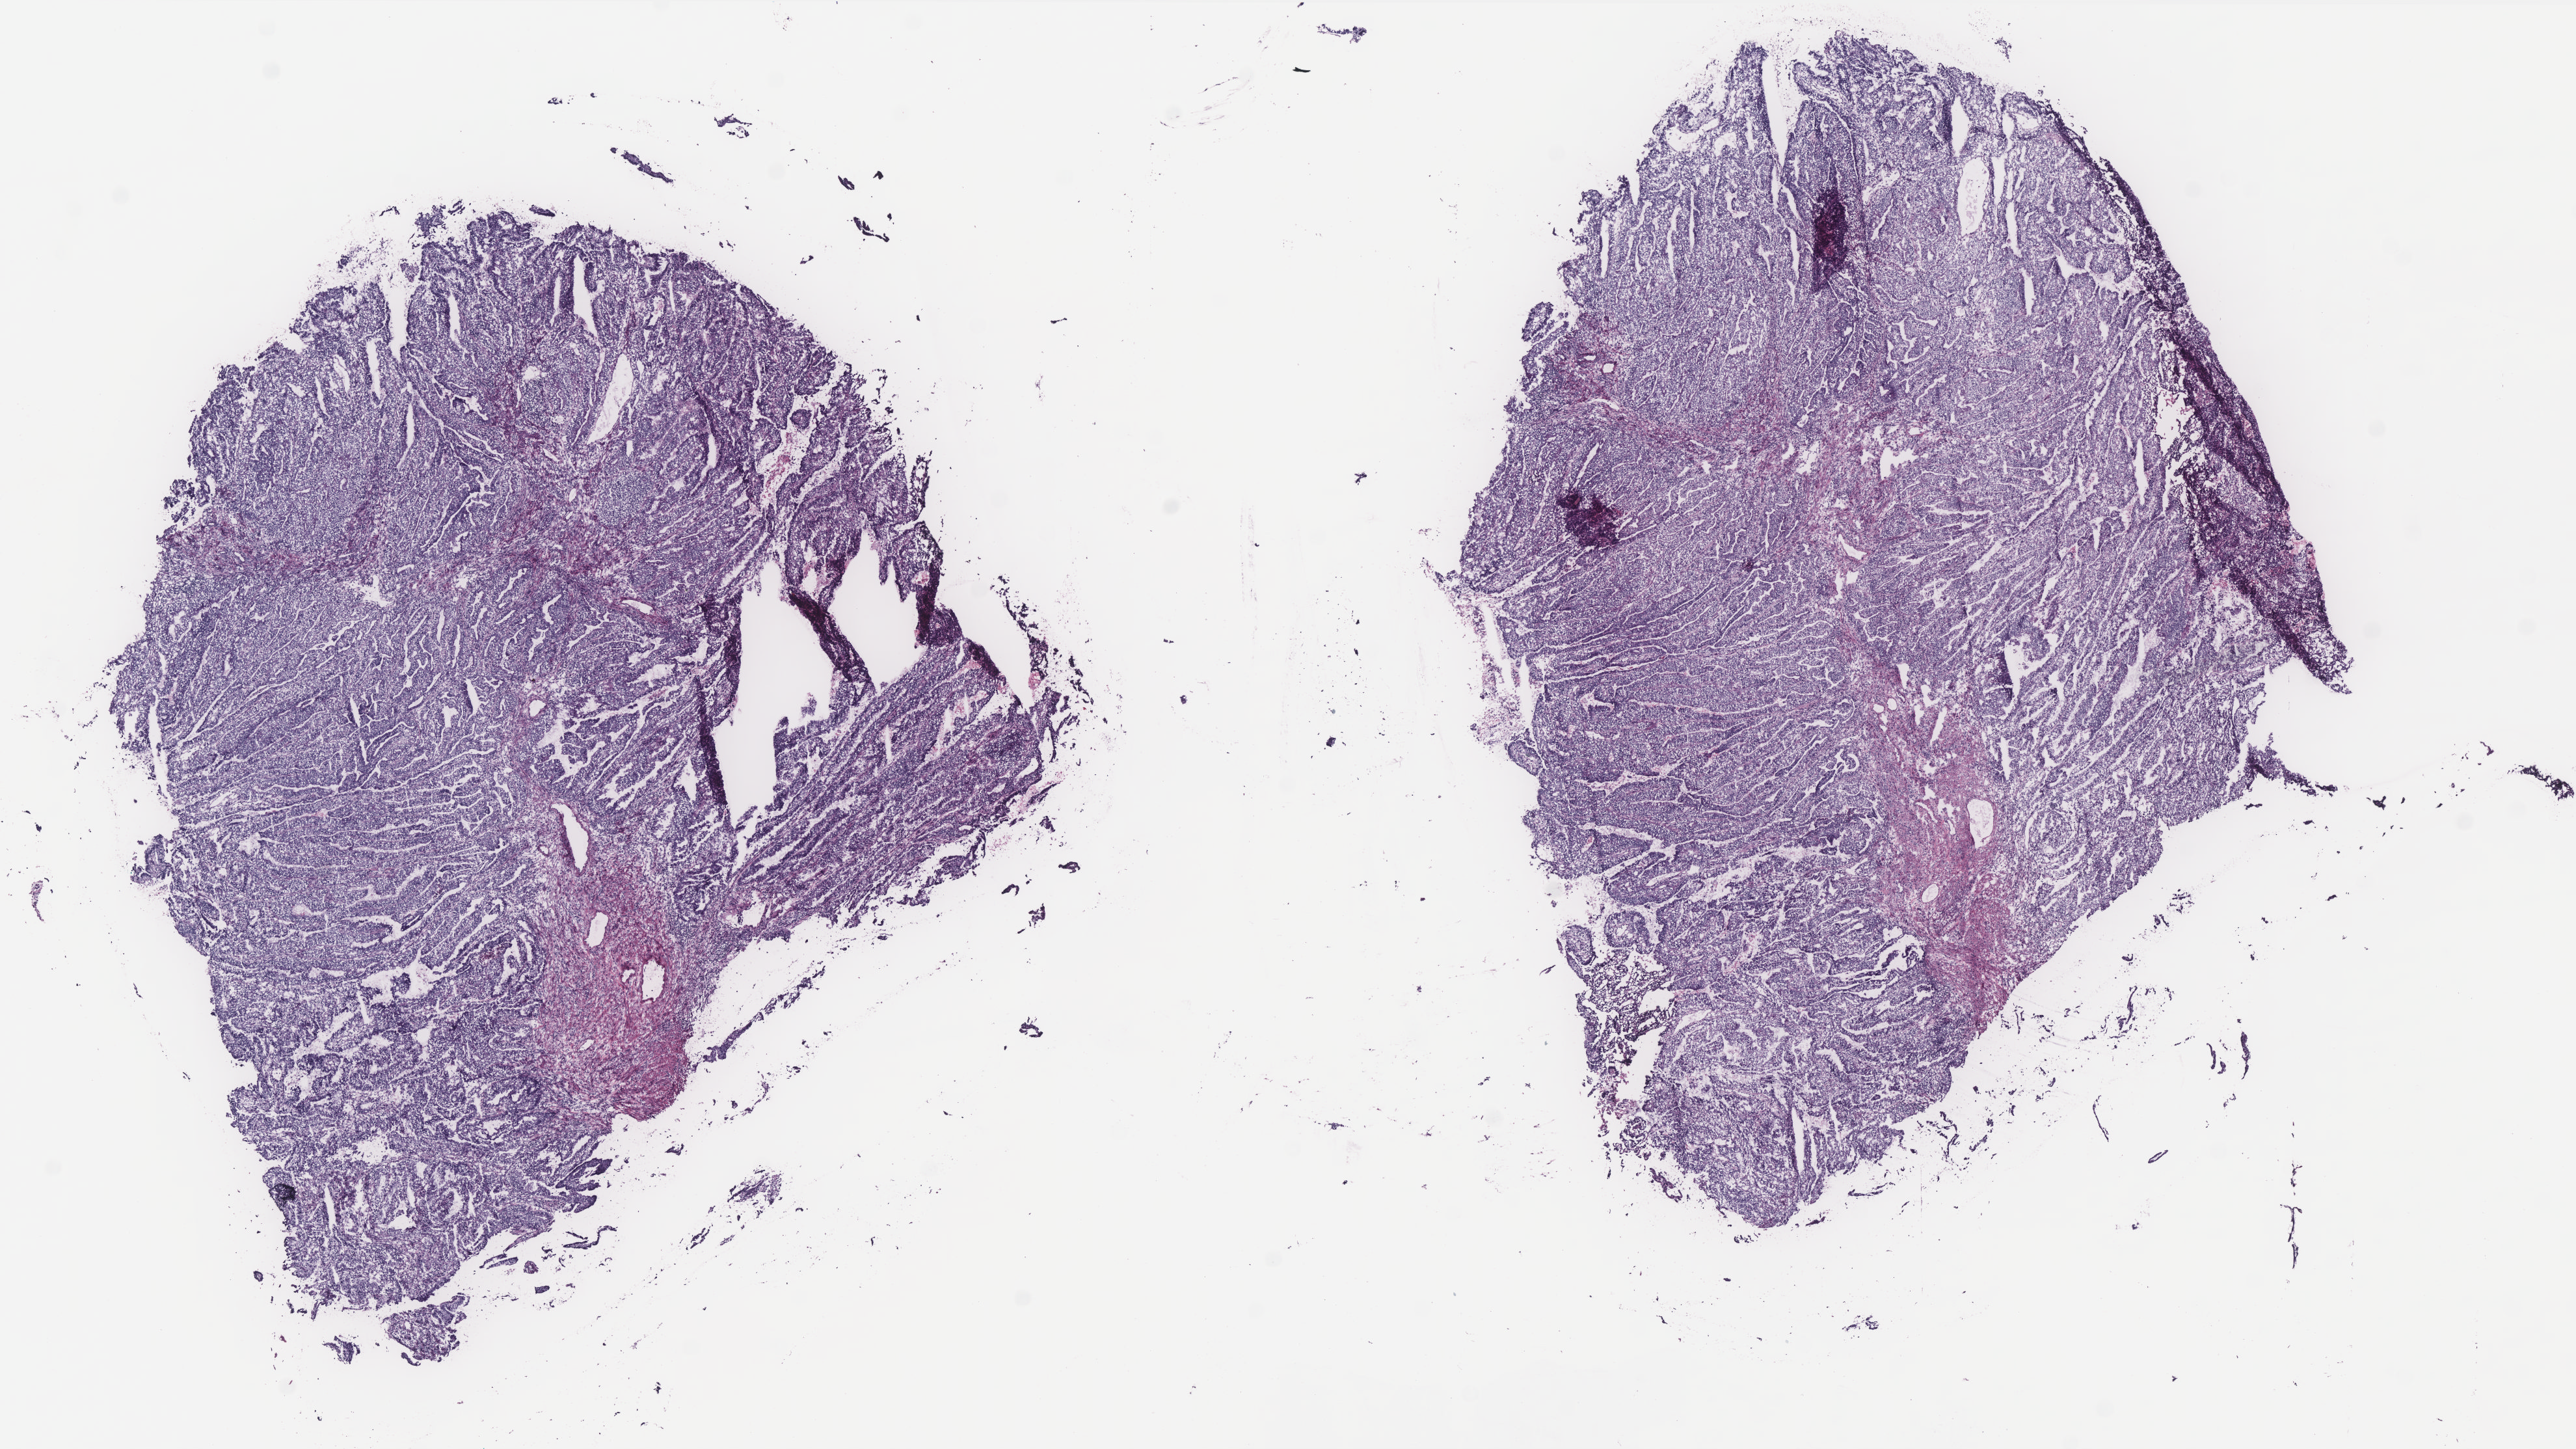
Whole-slide histology image, Hematoxylin and eosin (H&E) stained — shown as a low-resolution overview of the whole scanned area (about 15.9 x 8.9 mm, from a 40x scan), frozen section from the top of the tissue portion, sample: primary tumour, uterus. Patient: female, age at initial diagnosis 63 years. Histologic grade: G2 (moderately differentiated). Composition of this section per pathologist review: tumour cells 80%, tumour nuclei 80%, normal cells 0%, stromal cells 15%, necrosis 5%. Infiltration values recorded for this section: lymphocyte infiltration 30%, monocyte infiltration 20%, neutrophil infiltration 40%.
Pathologic diagnosis: Endometrioid adenocarcinoma, NOS (endometrium). FIGO stage: IC.